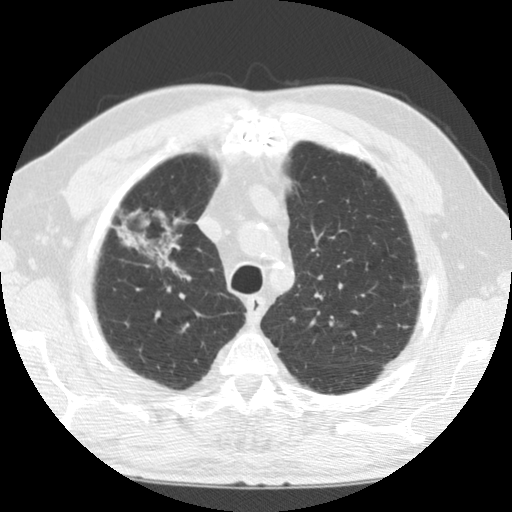
Low-dose screening chest CT, axial slice. First (baseline) screen. Lung window (W 1500 / L -600 HU). 512 × 512 image matrix, field of view 320 × 320 mm. Male, age 69 years at enrolment. Former smoker at enrolment.
Lesion marked by an expert reader, box from (x=102, y=207) to (x=198, y=292) px. No non-calcified nodule or mass ≥4 mm was recorded by the screening reader at this exam. Later outcome: lung cancer diagnosed 171 days after this screen — adenocarcinoma, NOS, right upper lobe, poorly differentiated (G3), stage IIIB (AJCC 6th edition), 40 mm at pathology.